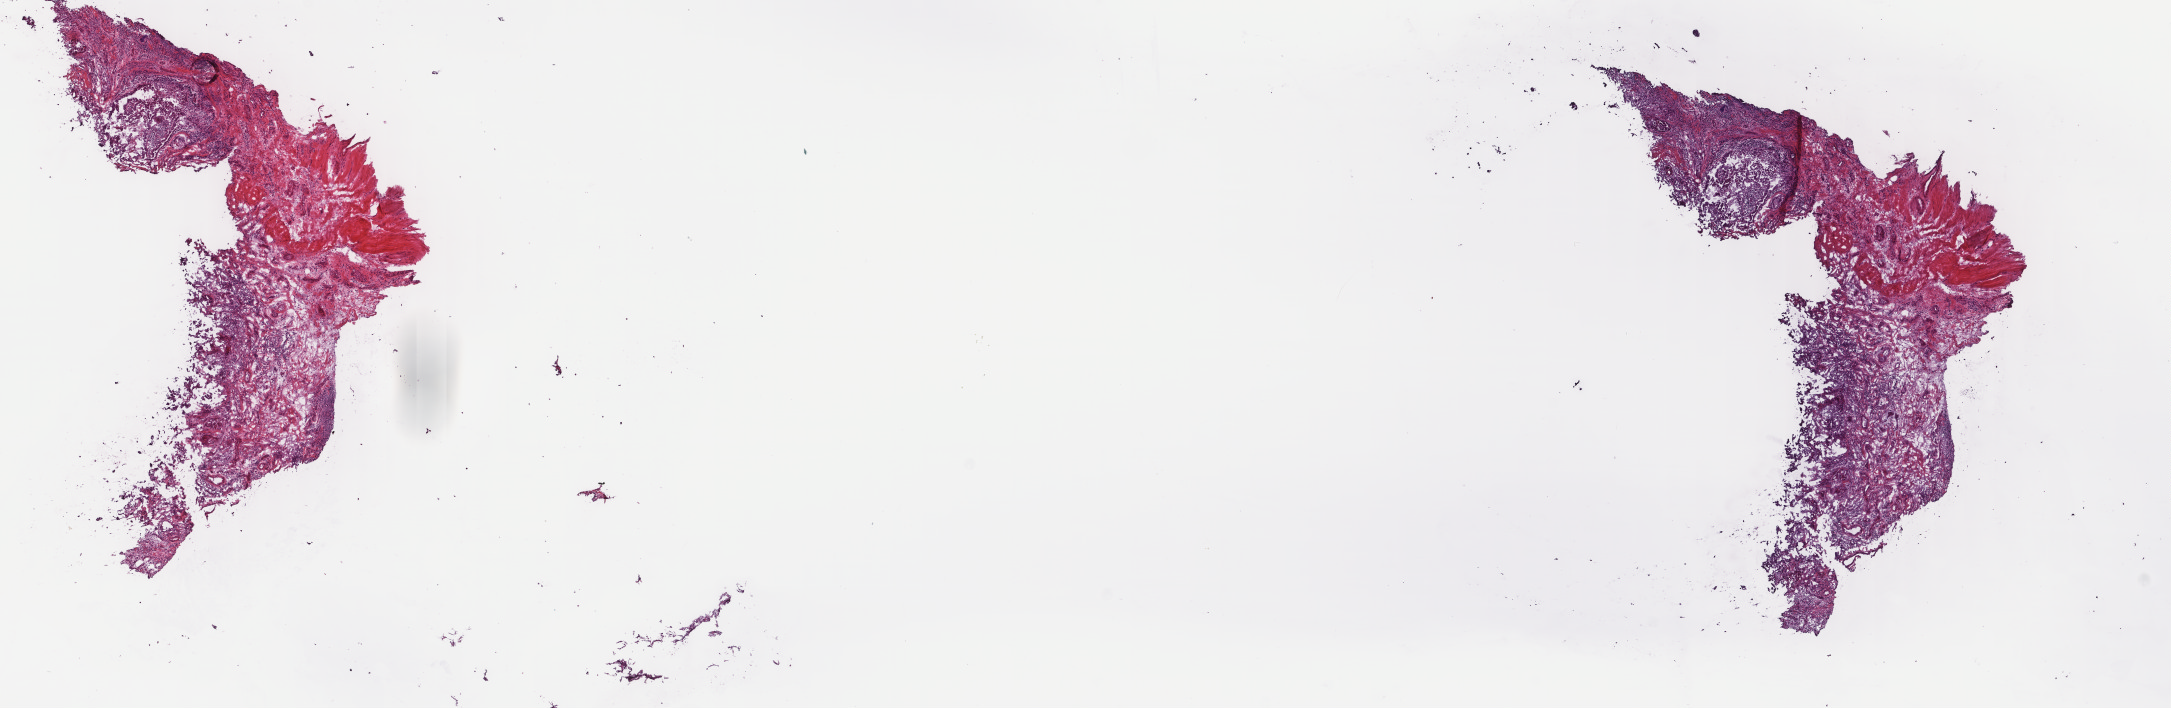
Hematoxylin and eosin (H&E) stained whole-slide image, a low-resolution overview of the entire scanned area, about 17.2 x 5.6 mm (from a 40x scan), frozen section, thyroid, primary tumour sample. Female, age 60 years at initial diagnosis. Composition of this section per pathologist review: tumour cells 60%, tumour nuclei 100%, normal cells 0%, stromal cells 40%, necrosis 0%. Inflammatory infiltration, as recorded: lymphocyte infiltration 10%, monocyte infiltration 0%, neutrophil infiltration 0%.
Histologic diagnosis: Papillary carcinoma, columnar cell (thyroid gland). TNM: T3 N1b M0. AJCC pathologic stage: IVA (7th edition). Lymph nodes positive (case pathology): 4 of 12 examined. Laterality: right.